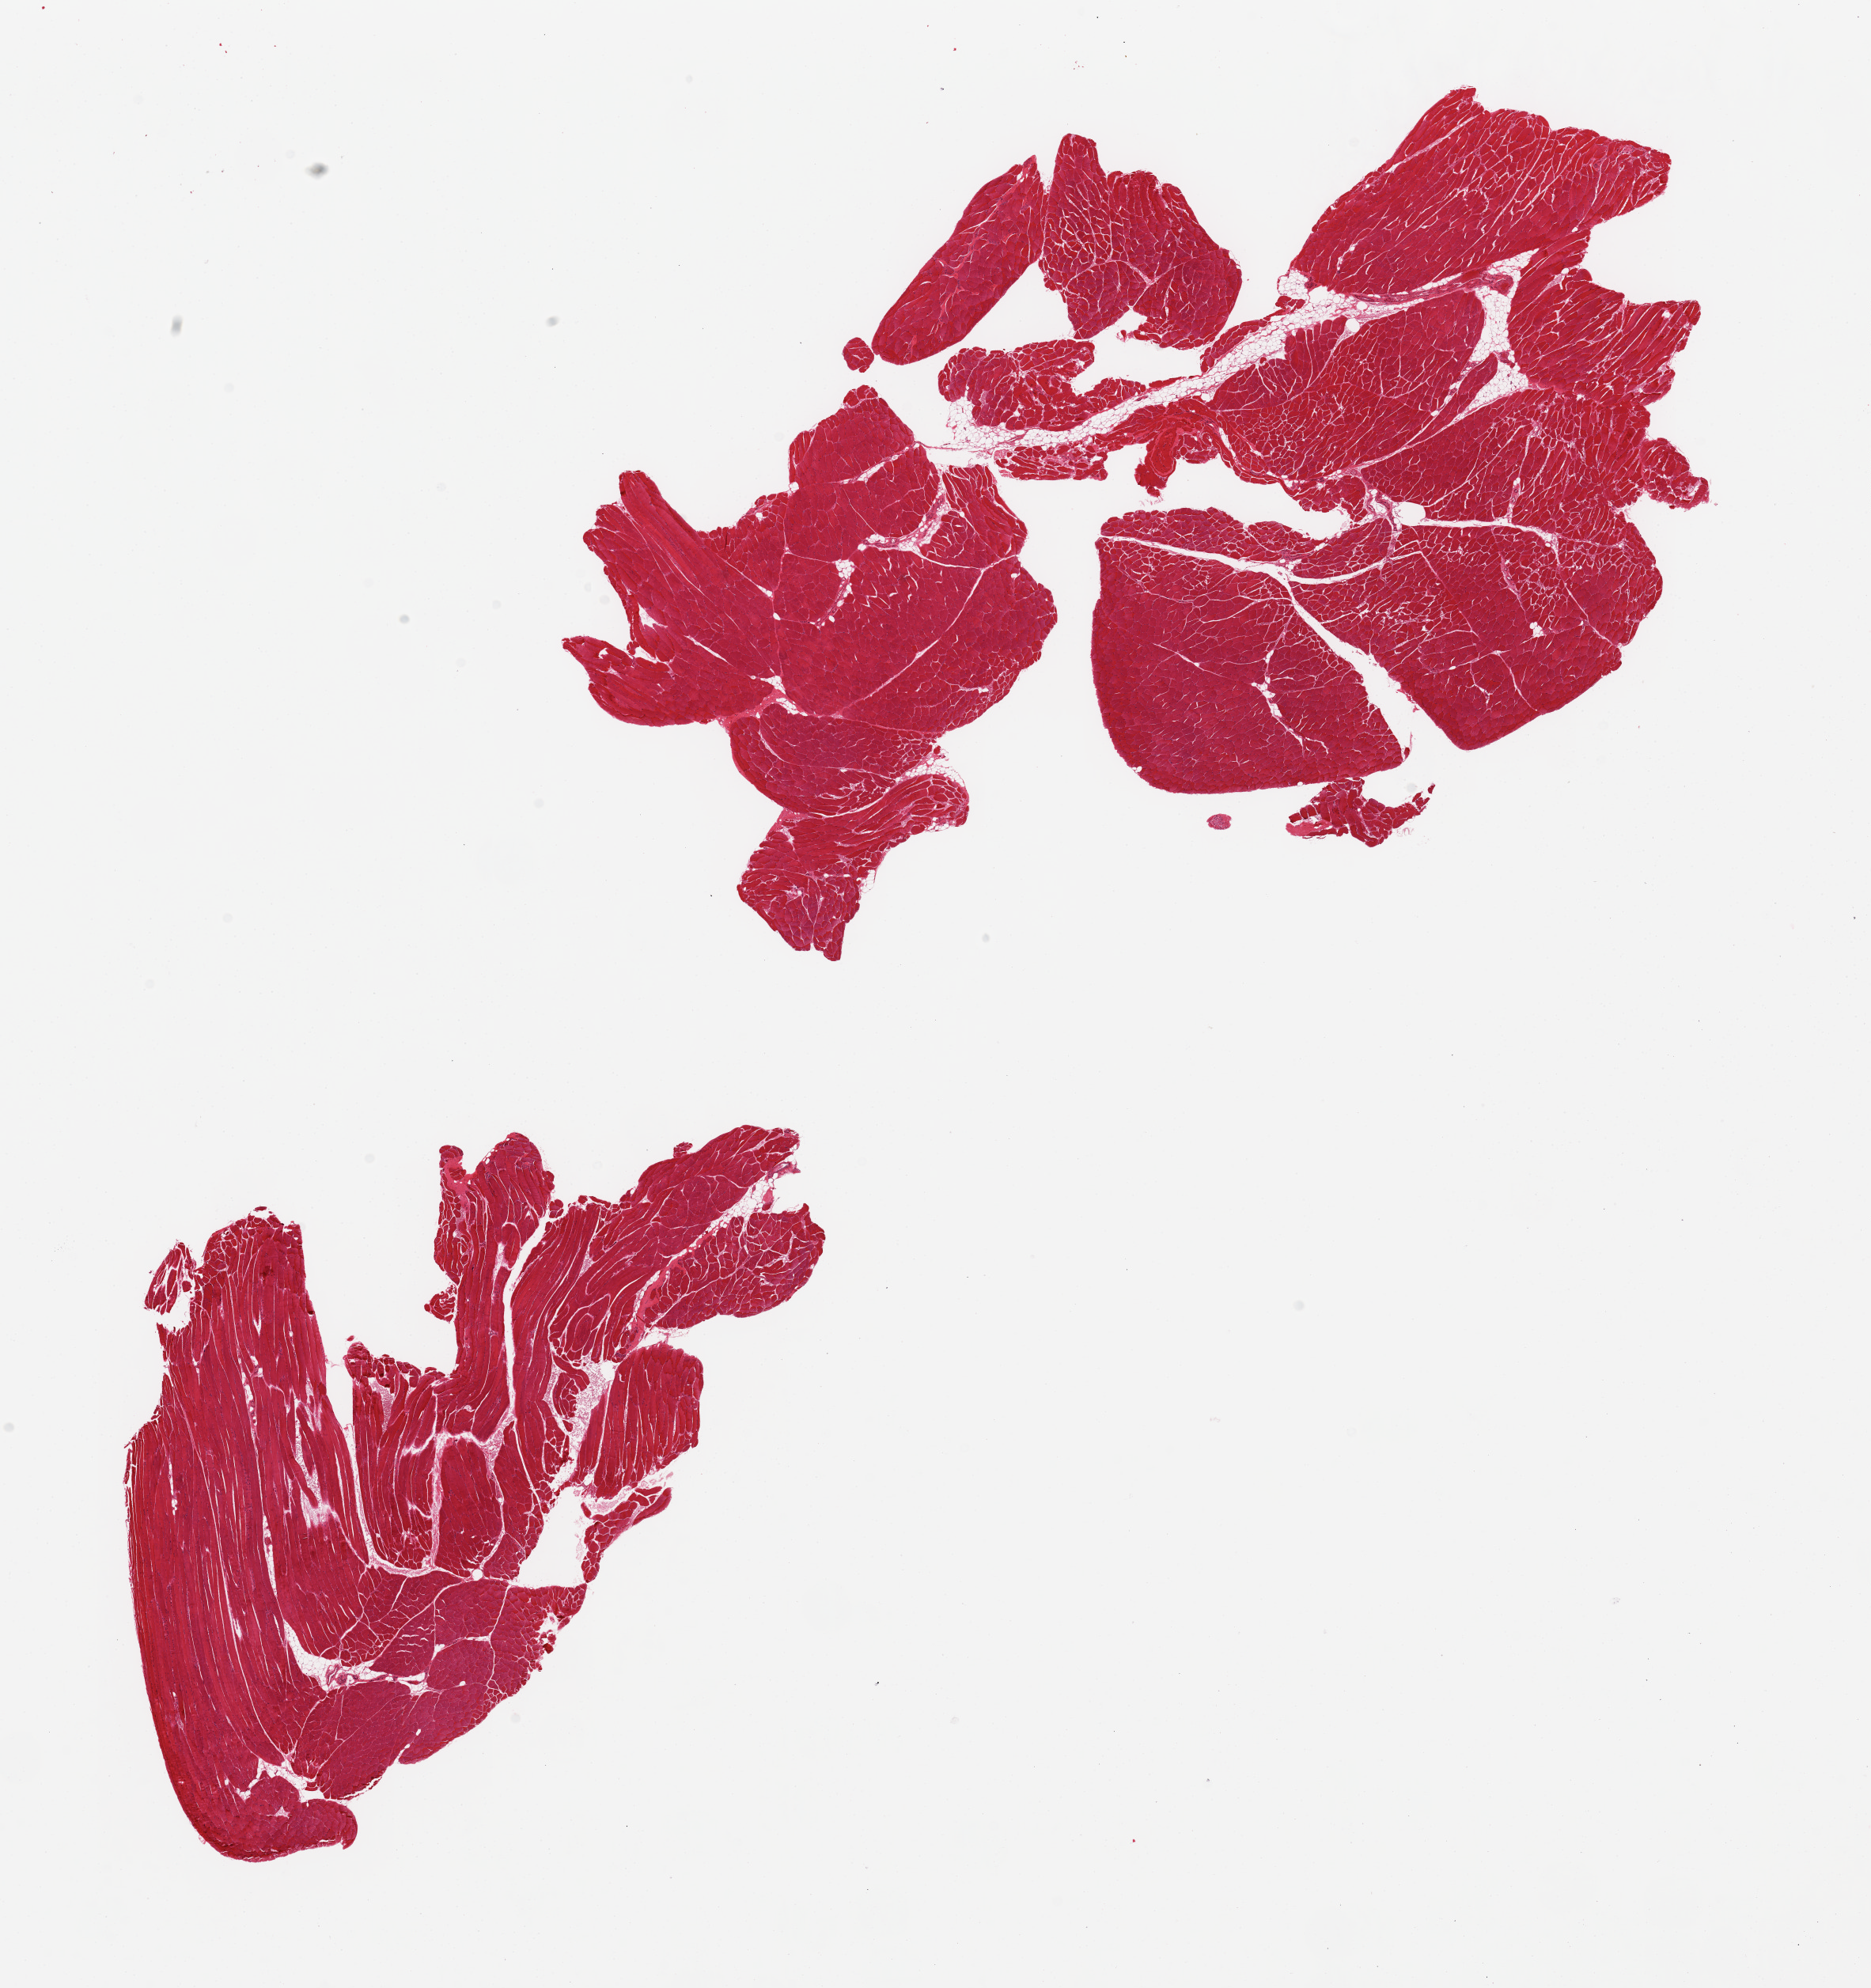
Digitized H&E-stained section — low-resolution overview of the scanned area, about 18.7 x 19.9 mm, PAXgene-fixed paraffin-embedded (PFPE) section, sampled site (target tissue): skeletal muscle, tissue donor sample. Male donor.
Reviewer comment on this tissue sample: 2 pieces; <10% internal fat.